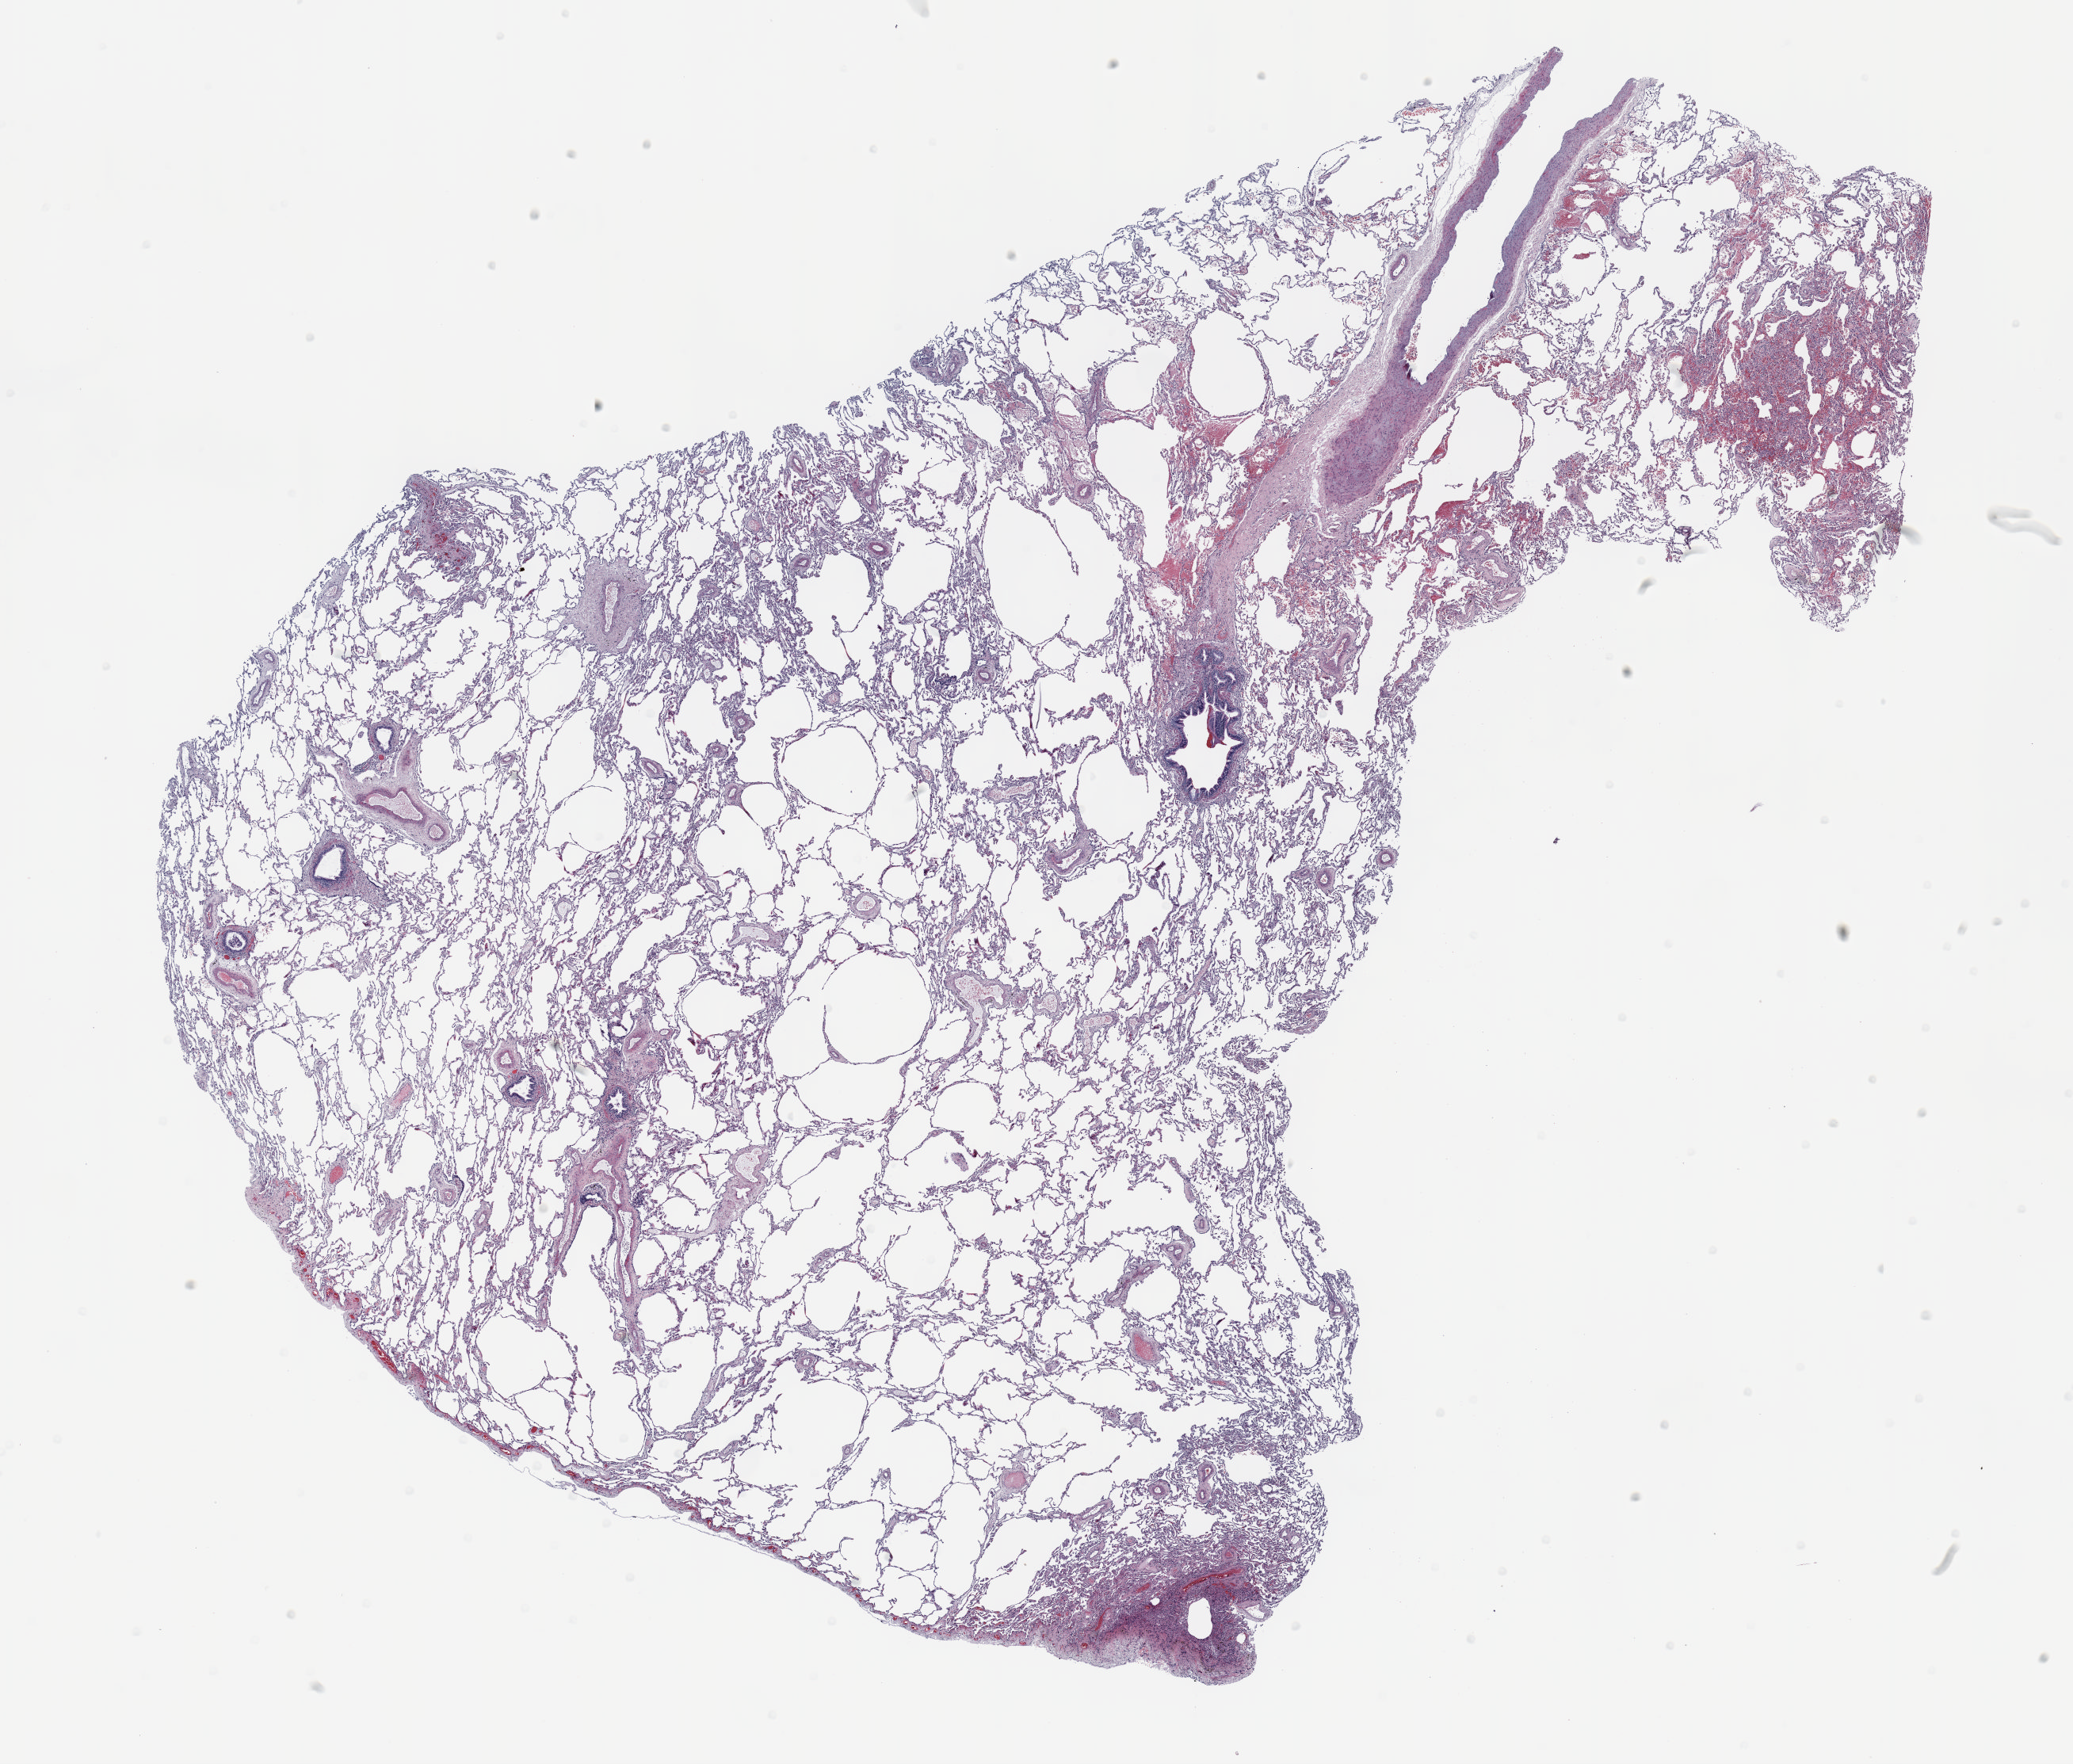
Hematoxylin and eosin (H&E) stained whole-slide image, low-resolution overview of the scanned area, about 21.0 x 17.9 mm, formalin-fixed paraffin-embedded (FFPE) section, lung. Male patient, aged 58 at enrolment.
Participant's lung-cancer diagnosis: Adenocarcinoma, NOS (ICD-O-3 8140/3).